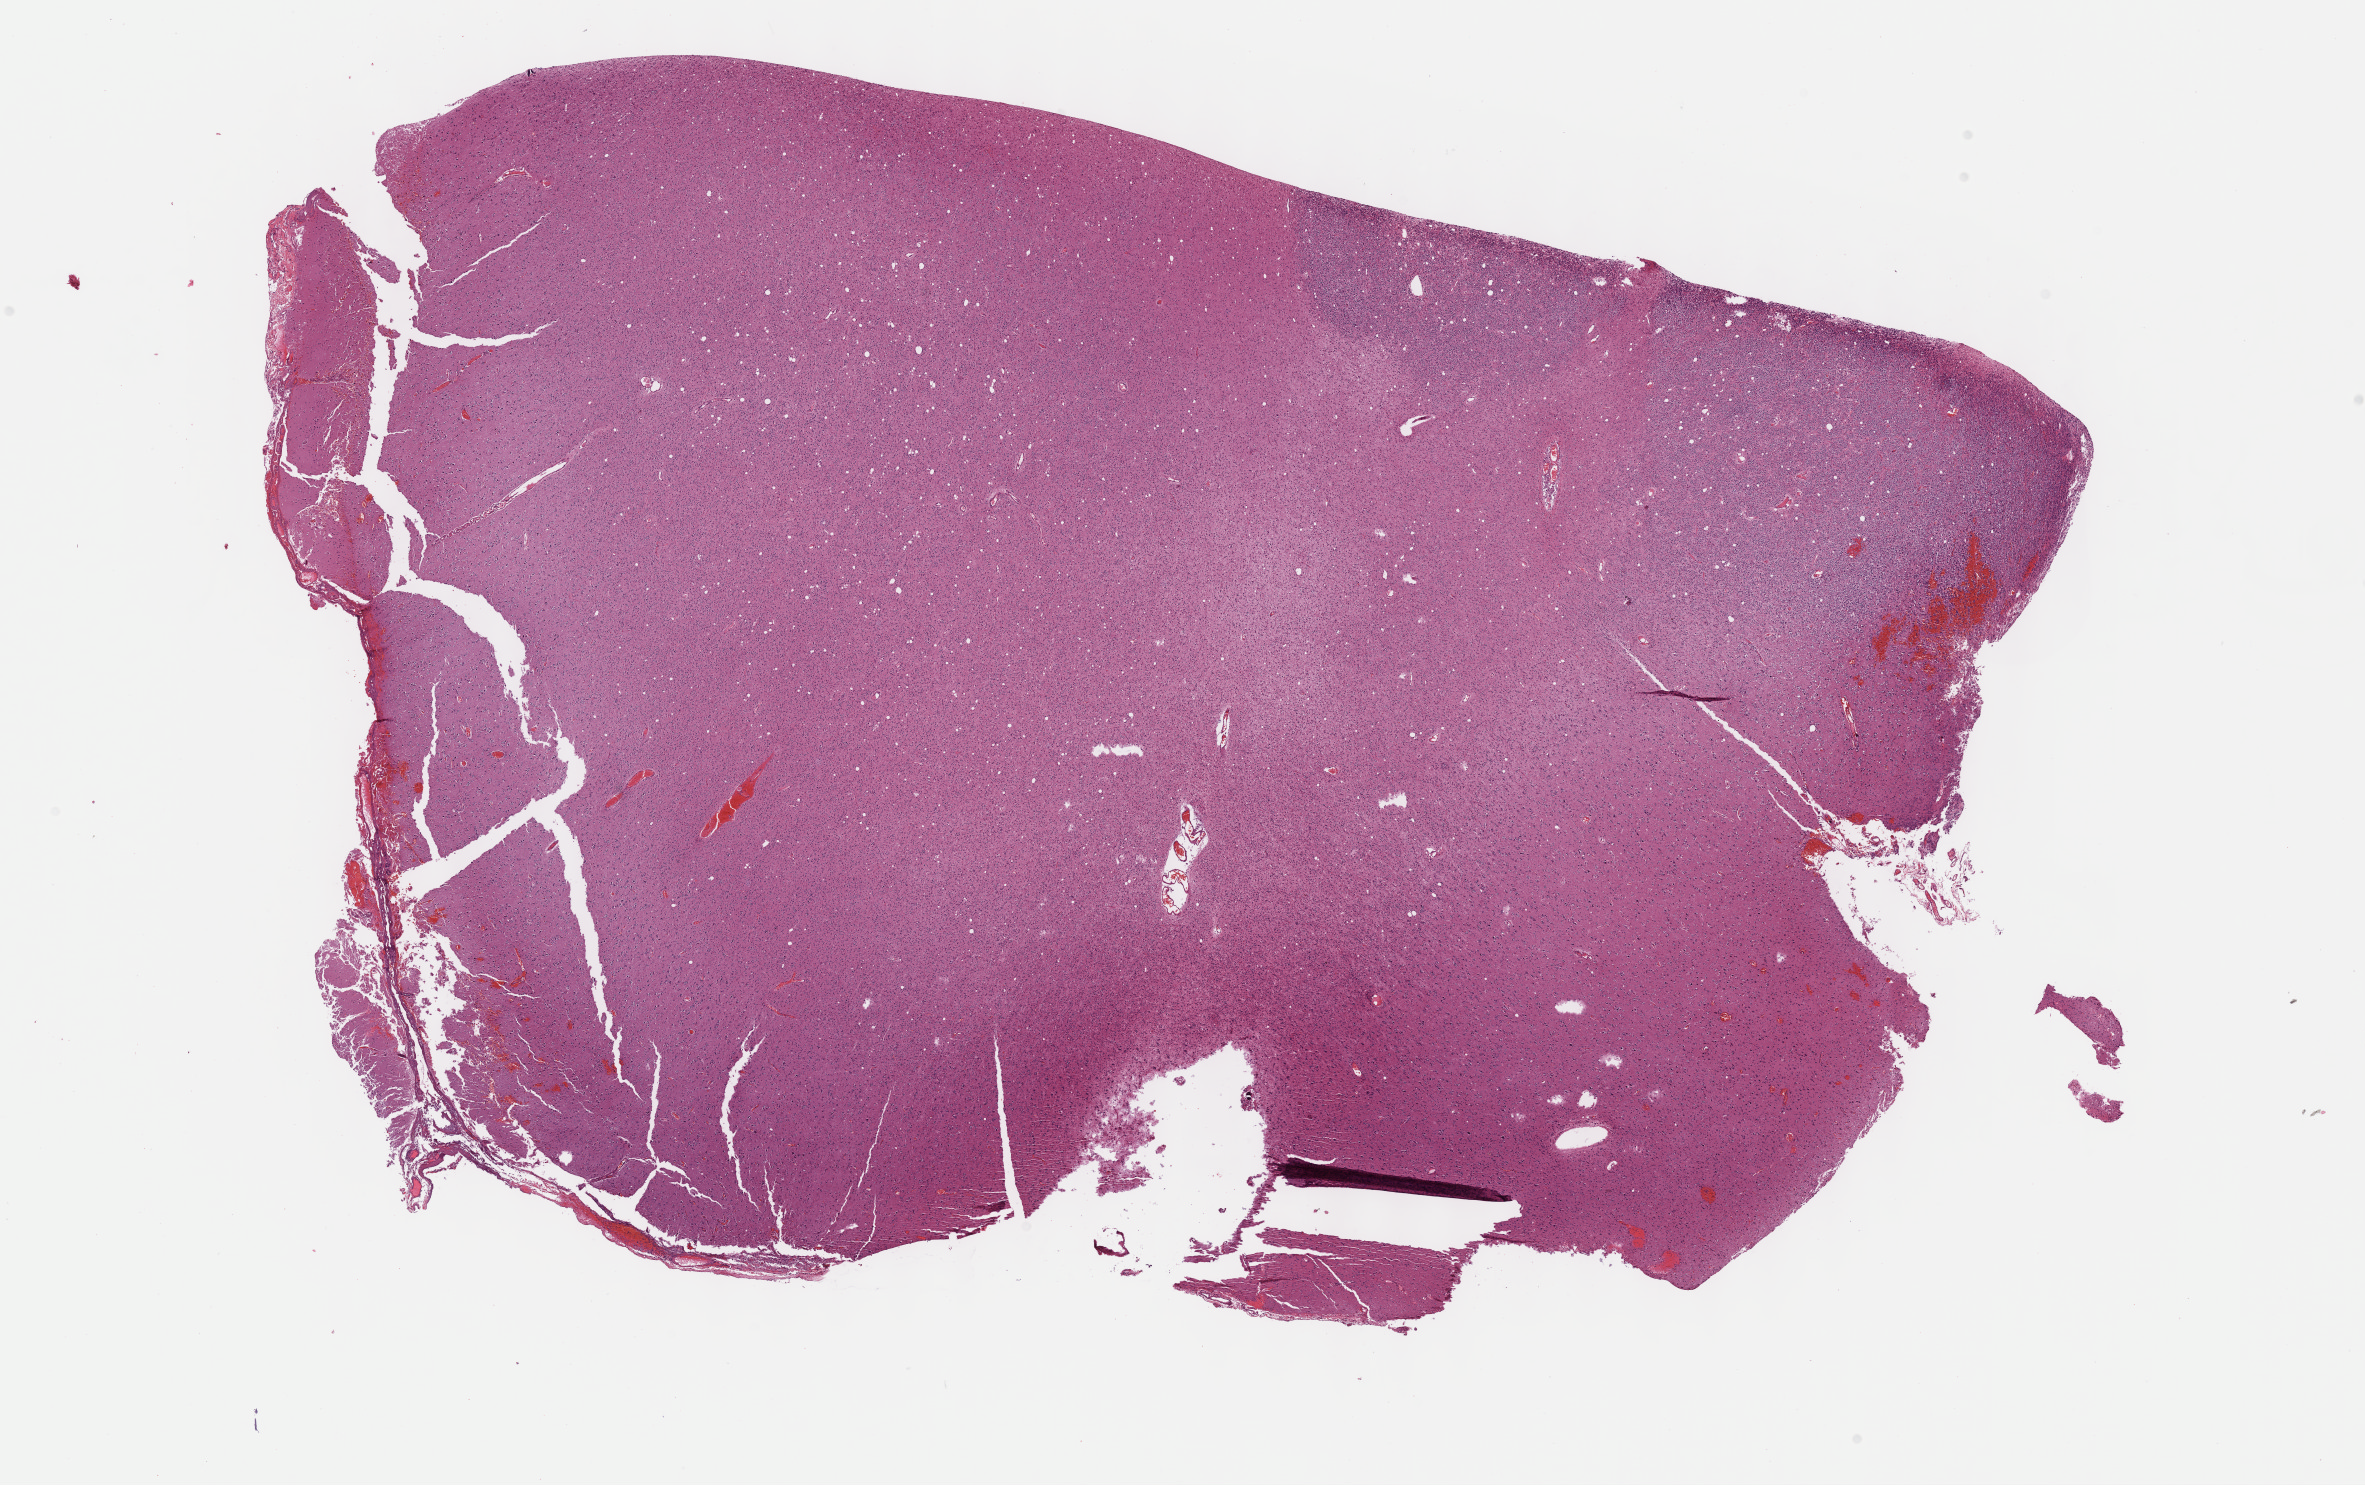
Hematoxylin and eosin (H&E) stained whole-slide image, low-resolution overview of the scanned area, about 19.1 x 12.0 mm (acquisition: 40x scan); formalin-fixed paraffin-embedded (FFPE) diagnostic section; brain, primary tumour sample. Male, age 40 years at initial diagnosis. Histologic grade: G3 (poorly differentiated).
Pathologic diagnosis: Oligodendroglioma, anaplastic. Laterality: left.